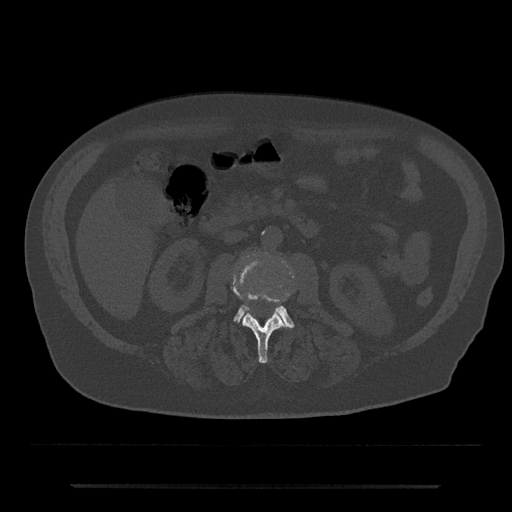
CT including the spine, one axial slice. Slice 447 of 797 in the series (ordered by position). 120 kVp. Bone window (W 1800 / L 400 HU). 0.5 mm slice thickness. 512 × 512 image matrix, field of view 434 × 434 mm. Male patient, age 80 years. Case-level facts recorded for this patient, not image findings: primary cancer: prostate; vertebrae with lytic lesions (as recorded): L1, T11.
Annotated regions visible in this slice (semi-automatic segmentation, software-assisted and operator-edited):
- L2 vertebra: box from (x=232, y=260) to (x=288, y=363) px
- L3 vertebra: (x=233, y=305)–(x=295, y=328)